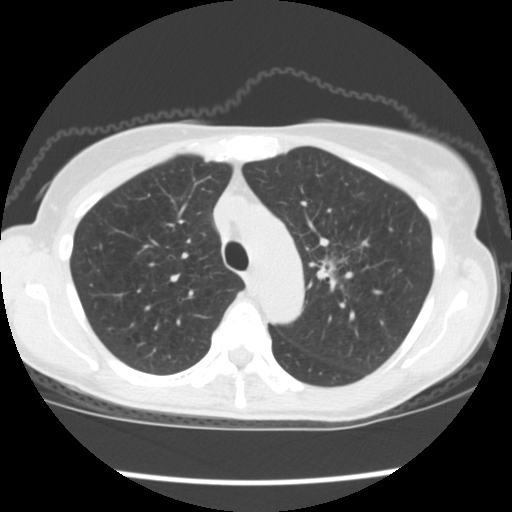
Chest CT (low-dose screening protocol), one axial image, baseline screening round, lung window (W 1500 / L -600 HU), standard (soft-tissue) reconstruction kernel (STANDARD), 120 kVp, slice 42 of 176 in the series. Female, age 67 years at enrolment. Former smoker at enrolment.
- Expert reader's lesion annotation, bounding box <307,233,382,312> (left, top, right, bottom; pixels).
- The exam's reader record, not a measurement of the box and not confirmed to be the same lesion: non-calcified nodule or mass ≥4 mm, left upper lobe, 34 × 32 mm, spiculated (stellate) margins, soft tissue attenuation, pre-existing on the prior screen: no.
- Lung cancer was diagnosed 17 days after this screen: small cell carcinoma, NOS, left upper lobe, stage IIIA (AJCC 6th edition), 40 mm at pathology.